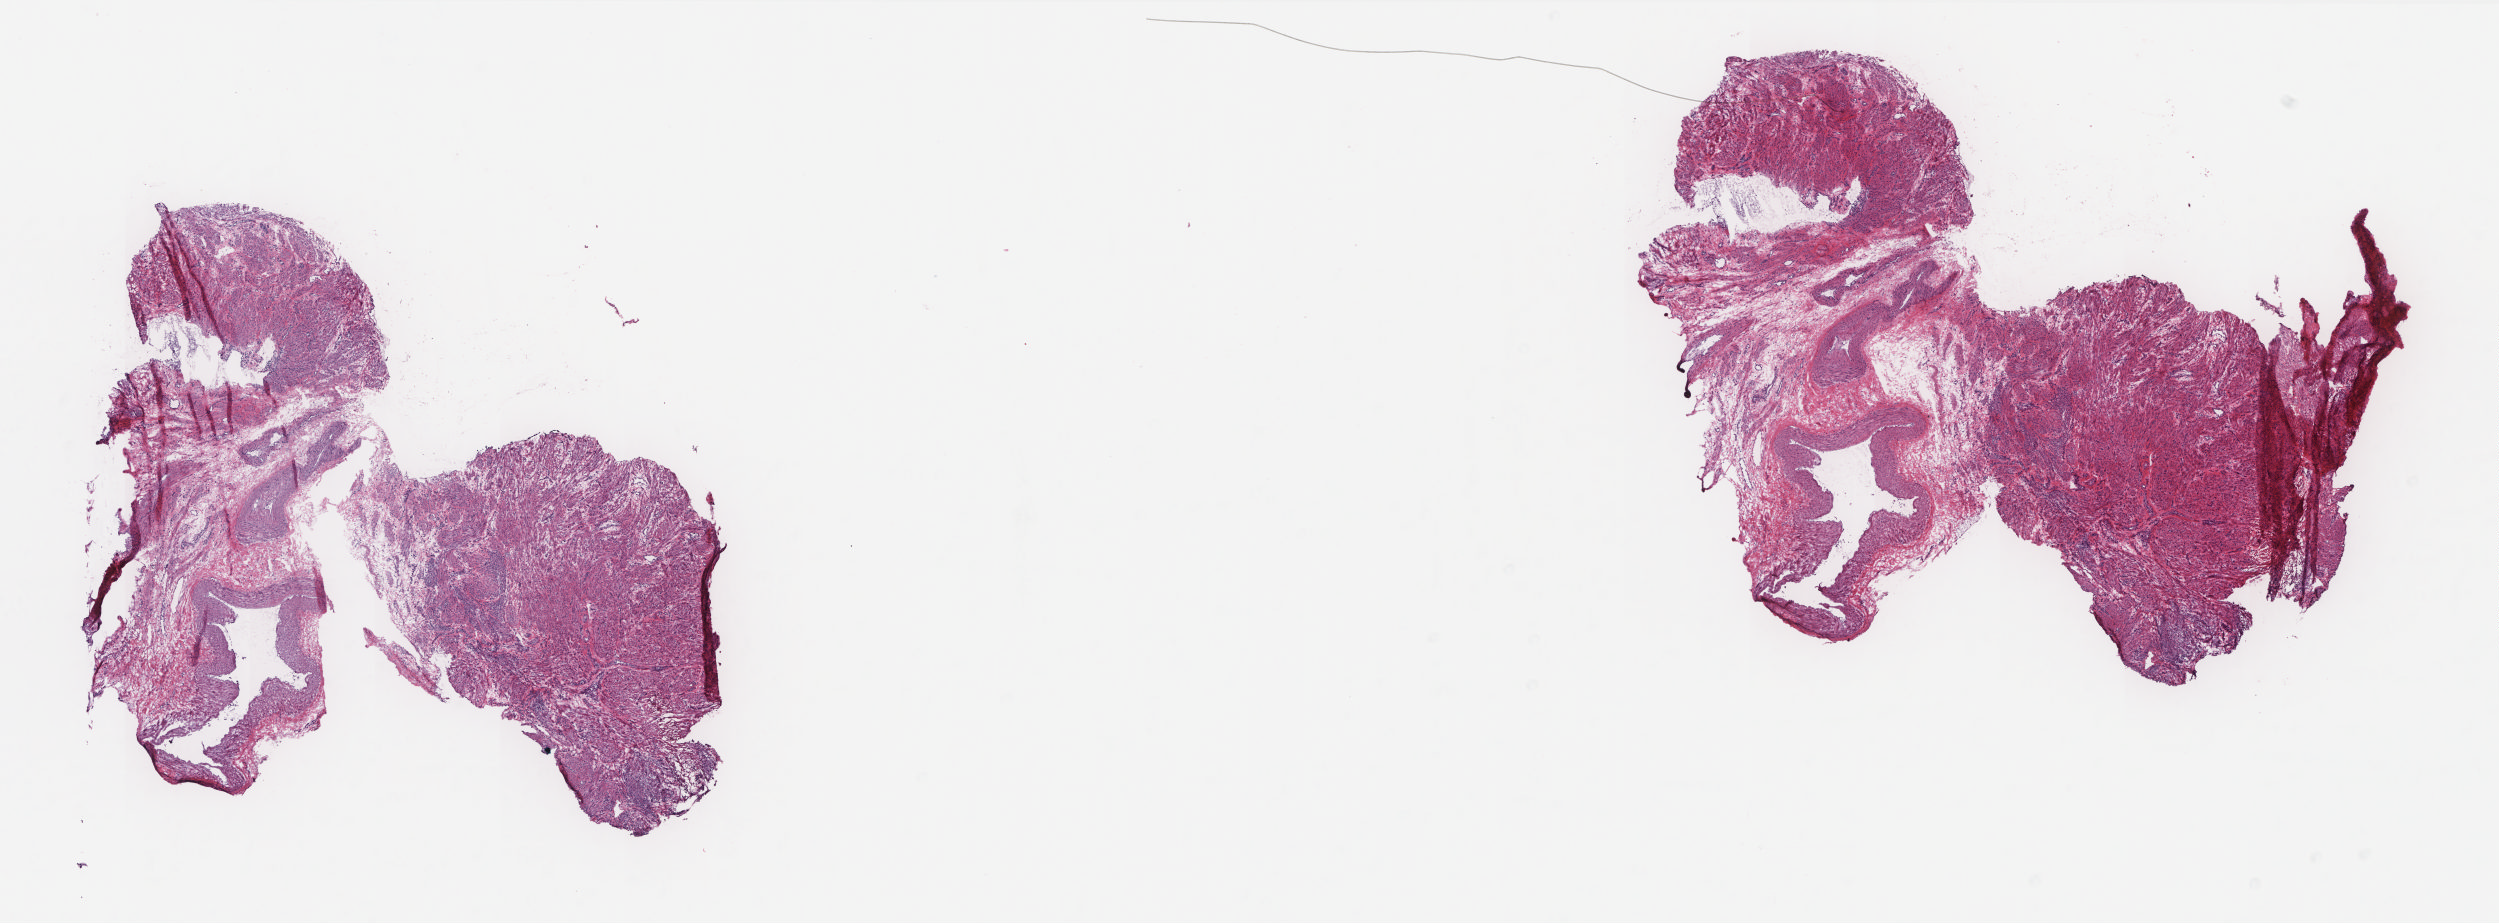
Hematoxylin and eosin (H&E) stained whole-slide image, whole scanned area (about 20.0 x 7.4 mm) shown as a low-resolution overview, frozen section from the top of the tissue portion, sample: solid tissue normal (non-tumour tissue), uterus. Female patient; age at initial diagnosis 47 years. Slide review estimates, as recorded: tumour cells 0%, tumour nuclei 0%, normal cells 100%, stromal cells 0%, necrosis 0%. Inflammatory infiltration, as recorded: lymphocyte infiltration 10%, monocyte infiltration 0%, neutrophil infiltration 0%.
This section: solid tissue normal sample (biorepository sample class). Patient diagnosis: Endometrioid adenocarcinoma, NOS (endometrium).